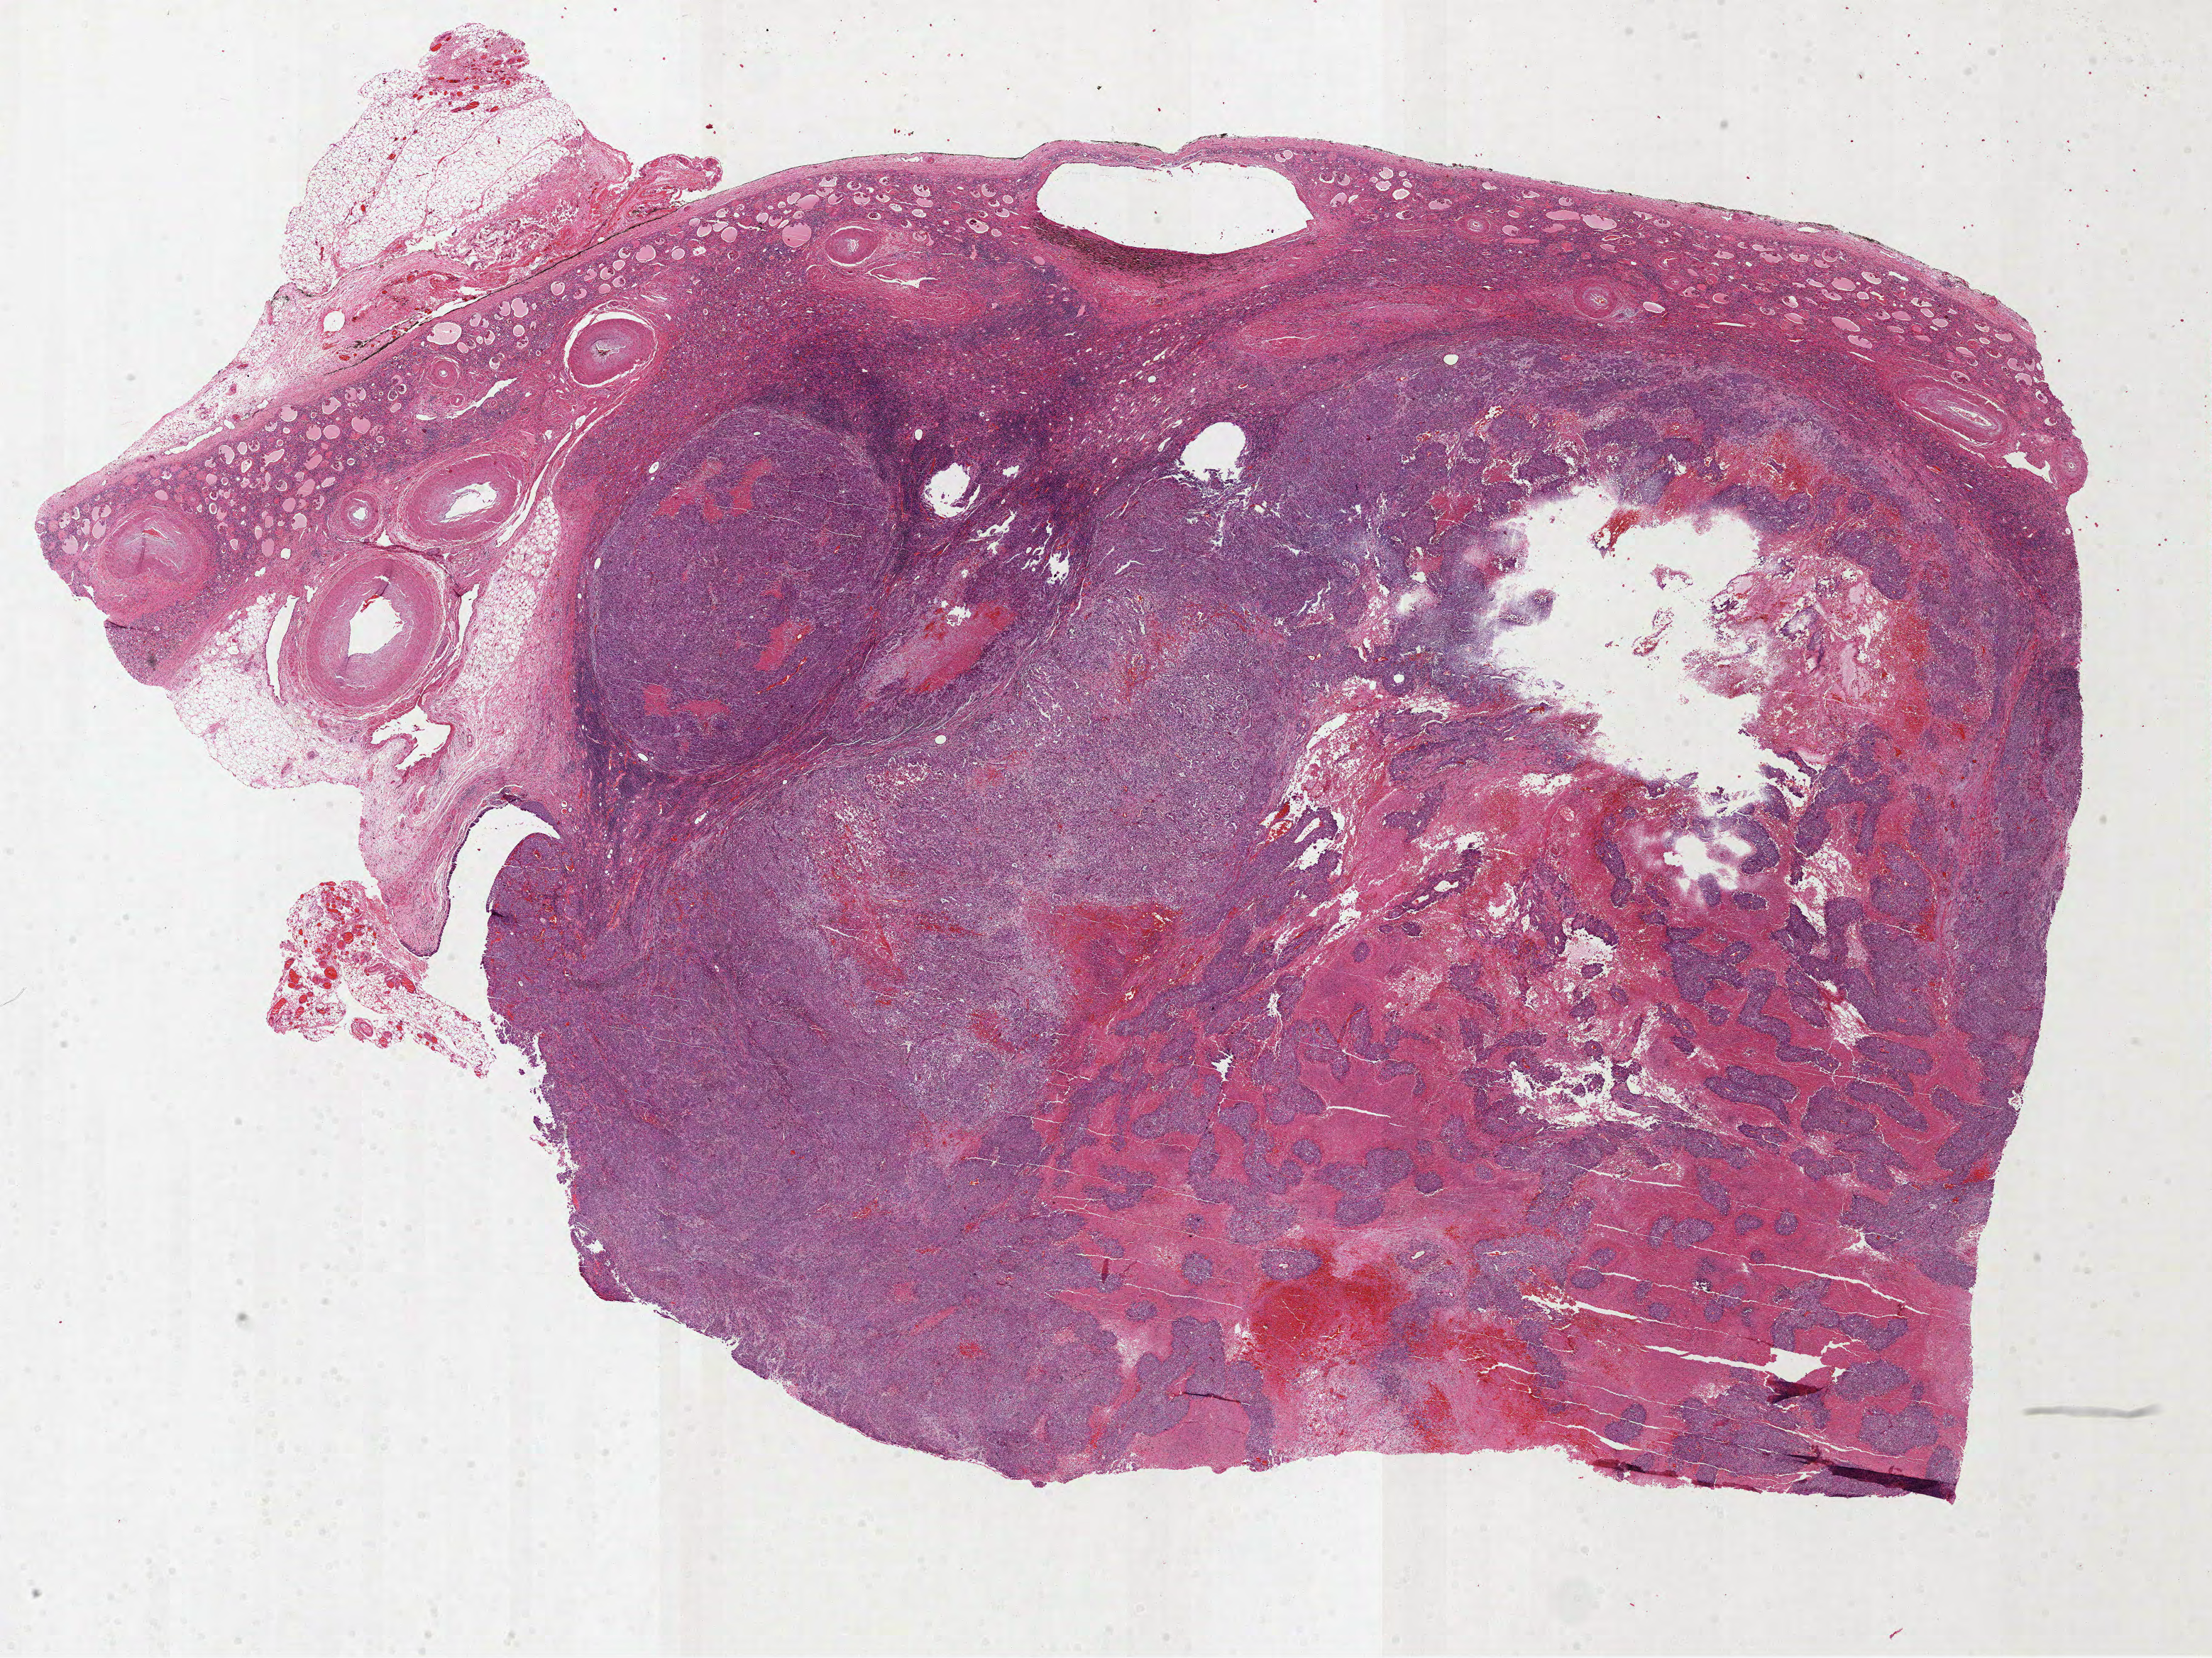
Whole-slide histology image, H&E, a low-resolution overview of the entire scanned area, about 25.1 x 18.8 mm (slide scanned at 40x); formalin-fixed paraffin-embedded (FFPE) diagnostic section; sample: primary tumour, kidney. Female patient; age at initial diagnosis 53 years.
Pathologic diagnosis: Clear cell adenocarcinoma, NOS.